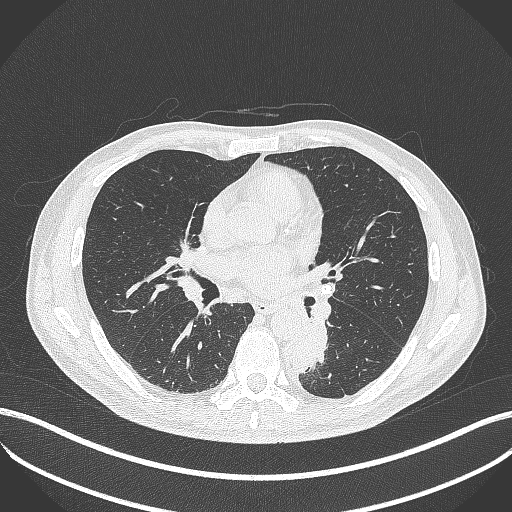
Chest CT, one axial slice. 120 kVp. Lung window (W 1500 / L -600 HU). 512 × 512 image matrix. Patient: male, 72 years. Case-level facts recorded for this patient, not image findings: clinical TNM (as recorded): T2b N0 M1.
Annotated regions visible in this slice (bounding box drawn by a radiologist):
- lung tumour (recorded histology: adenocarcinoma): box from (x=283, y=317) to (x=340, y=377) px